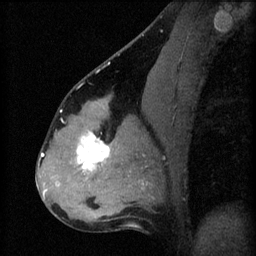
Breast MRI (dynamic contrast-enhanced), one sagittal slice. Position 32 of 60 along the scan axis. 3 images stored at this slice position (order not interpretable as contrast timing). 1.5 T. TE 4.2 ms, TR 8.2 ms. 256 × 256 image matrix. Patient: female, 37 years.
Structures marked on this image (semi-automatic segmentation, software-assisted and operator-edited):
- analysis volume of interest (the breast-tissue region the enhancement analysis was run in; not a lesion): bounding box [x1, y1, x2, y2] px = [67, 120, 122, 179]
- tumour enhancement mask (voxels above the 70 % enhancement threshold inside the analysis volume of interest): [76, 132, 110, 171]